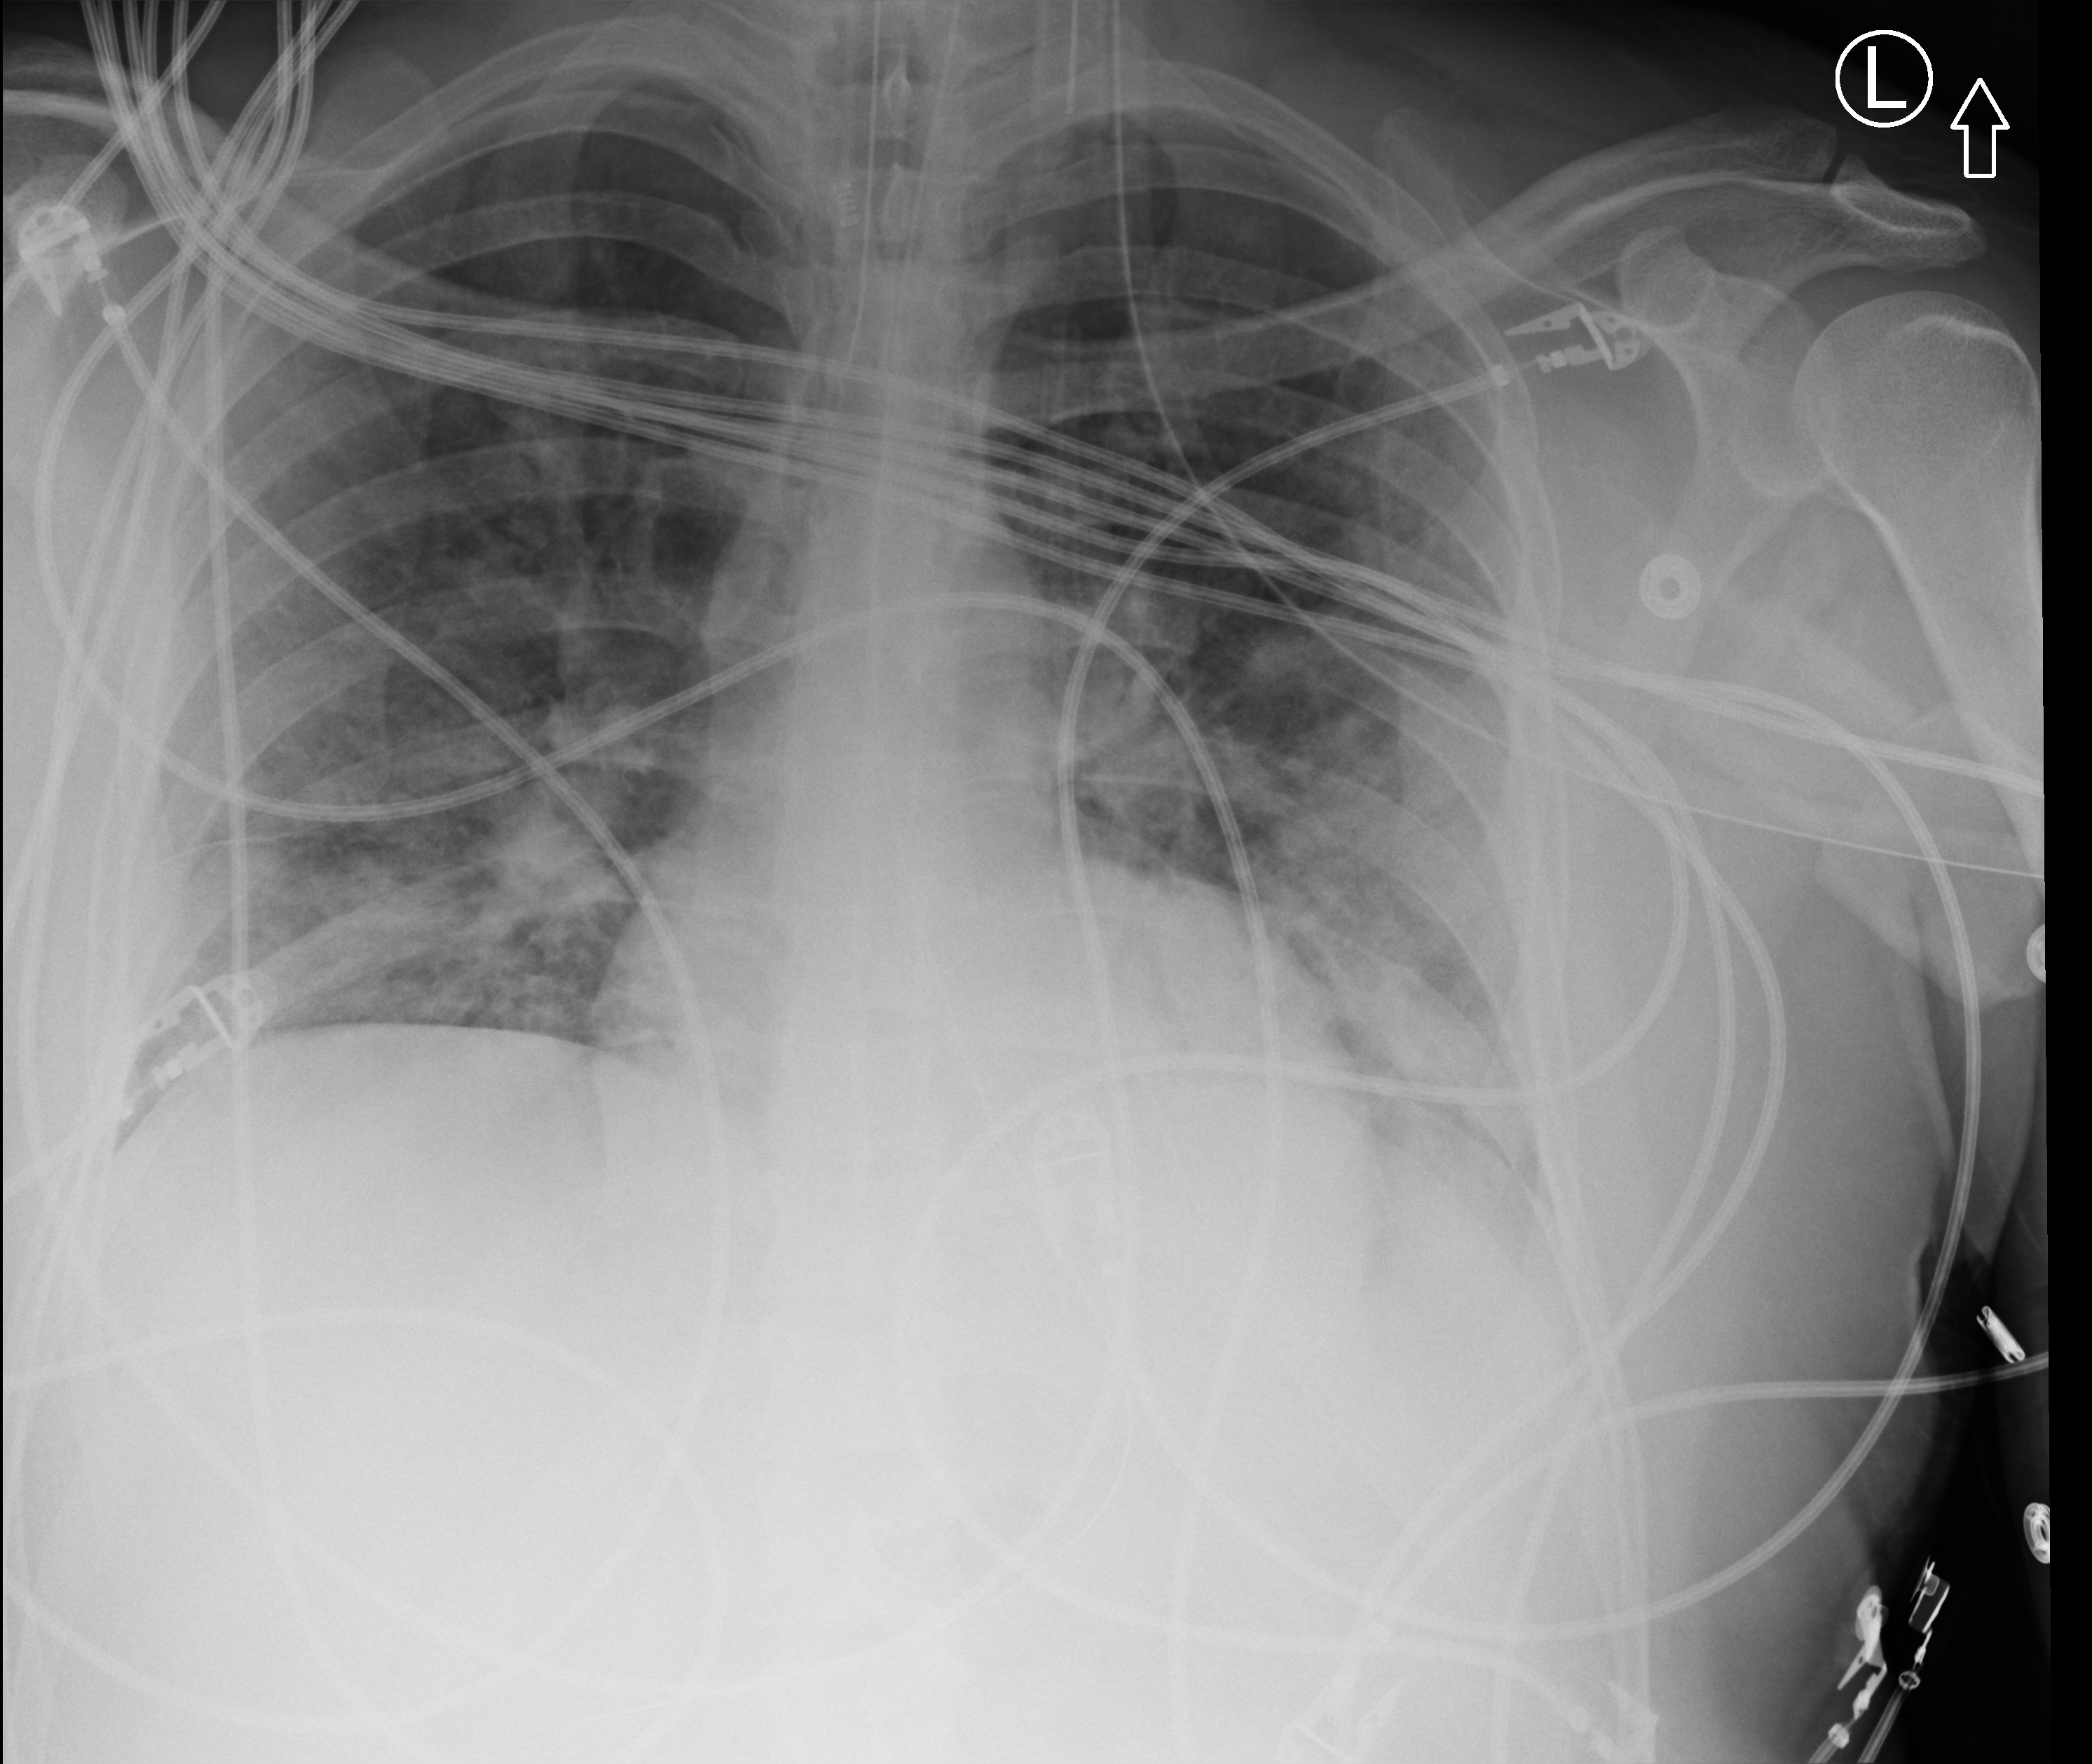
Portable chest radiograph. Male patient hospitalised with COVID-19, age 18–59 years.
Hospital-stay facts (about this admission, not read from this image; timing relative to this image not recorded):
- admitted to intensive care during this hospital stay: yes